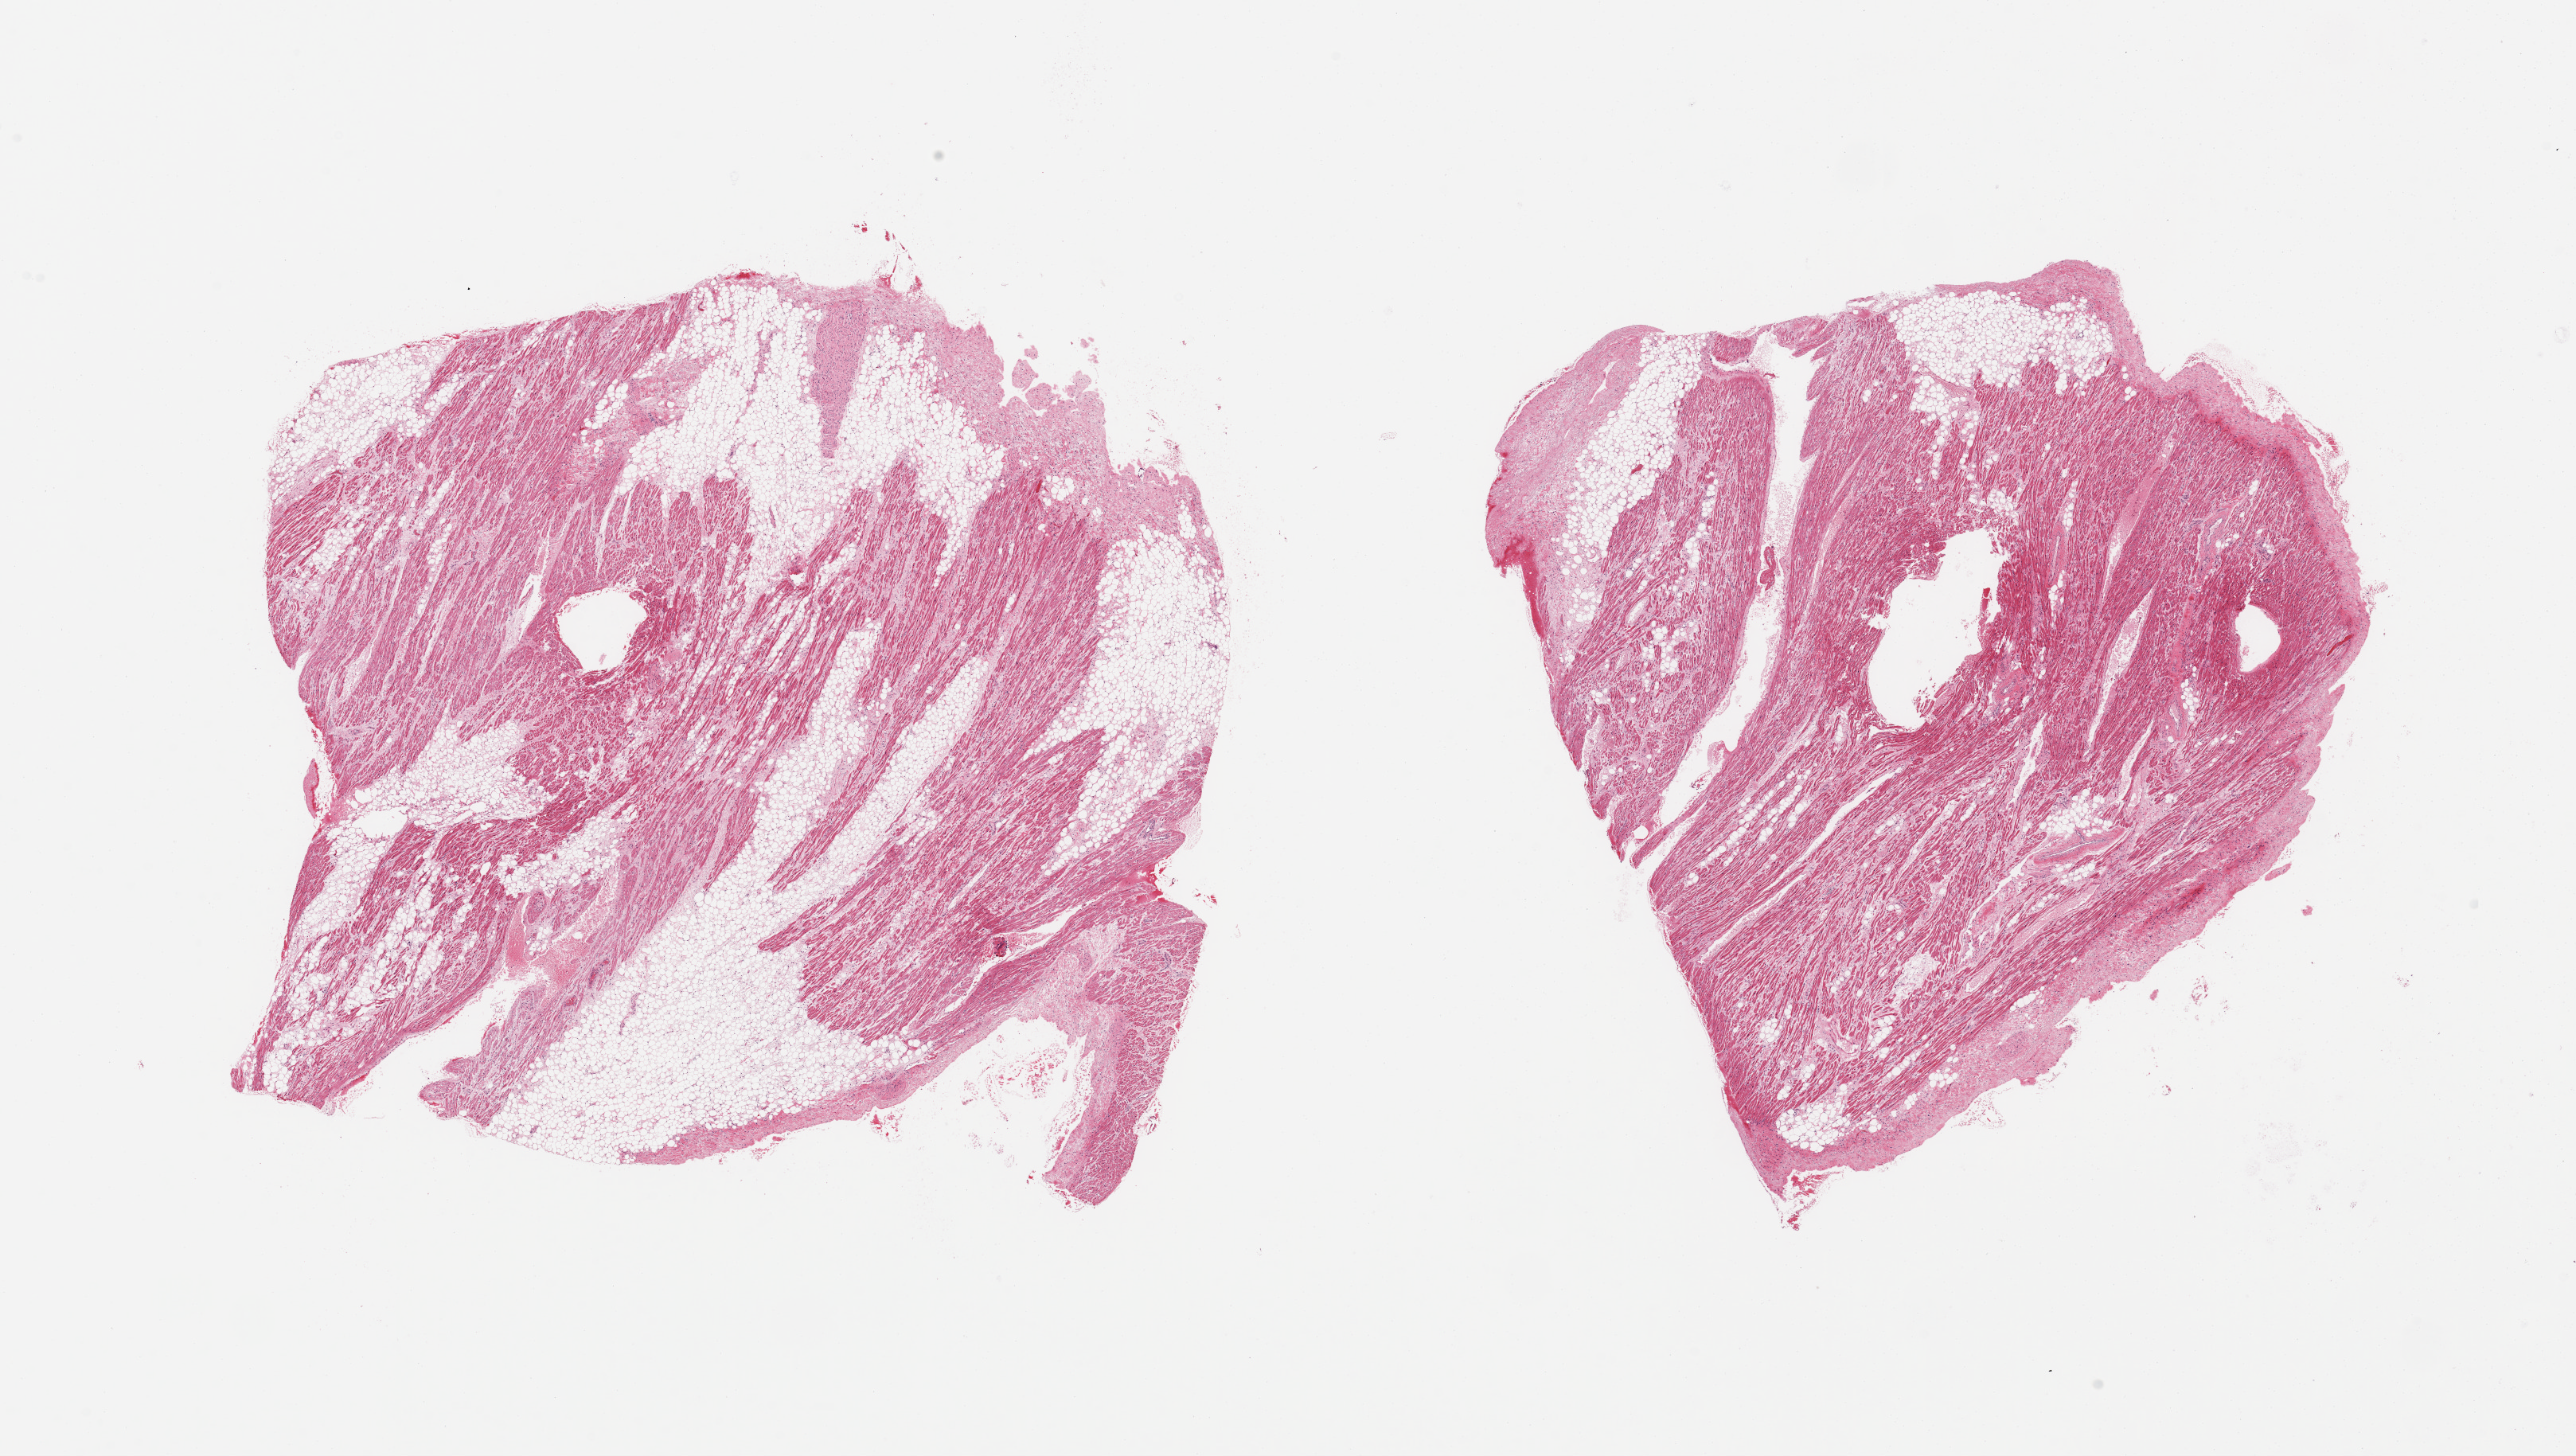
H&E whole-slide image, brightfield, a low-resolution overview of the entire scanned area, about 25.6 x 14.5 mm, PAXgene-fixed, paraffin-embedded tissue, section of auricular appendage (target tissue), donor tissue sample. Donor sex: female.
Reviewer comment on this tissue sample: 2 pieces, no abnormalities.